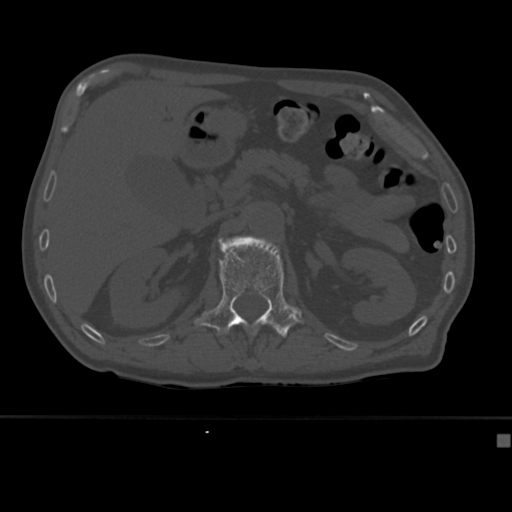
CT including the spine, one axial slice; slice 172 of 430 in the series (ordered by position); reconstruction kernel Br40s; 120 kVp; bone window (W 1800 / L 400 HU); 1.5 mm slice thickness; 512 × 512 image matrix. Male patient, age 64 years. From the clinical record (not read from this slice): primary cancer: uterus; vertebrae with lytic lesions (as recorded): T1, T4, T5, T7, L5.
Outlined on this slice (semi-automatic segmentation, software-assisted and operator-edited):
- L1 vertebra: bounding box [x1, y1, x2, y2] px = [194, 235, 303, 337]